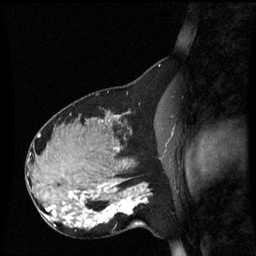
Breast MRI (dynamic contrast-enhanced), one sagittal slice; position 32 of 60 along the scan axis; dynamic contrast-enhanced series, image 2 of 3 at this slice position (ordered by acquisition); 1.5 T; TE 4.2 ms, TR 8.9 ms; 256 × 256 image matrix, field of view 220 × 220 mm. Patient: female, 31 years. From the clinical record (not read from this slice): setting: breast cancer imaged before/during neoadjuvant chemotherapy; receptor status: HR-positive, HER2-negative.
Annotated regions visible in this slice (semi-automatically segmented with operator editing):
- analysis volume of interest (the breast-tissue region the enhancement analysis was run in; not a lesion): bounding box (x1, y1, x2, y2) in pixels: (90, 180, 152, 229)
- tumour enhancement mask (voxels above the 70 % enhancement threshold inside the analysis volume of interest): (90, 182, 148, 229)